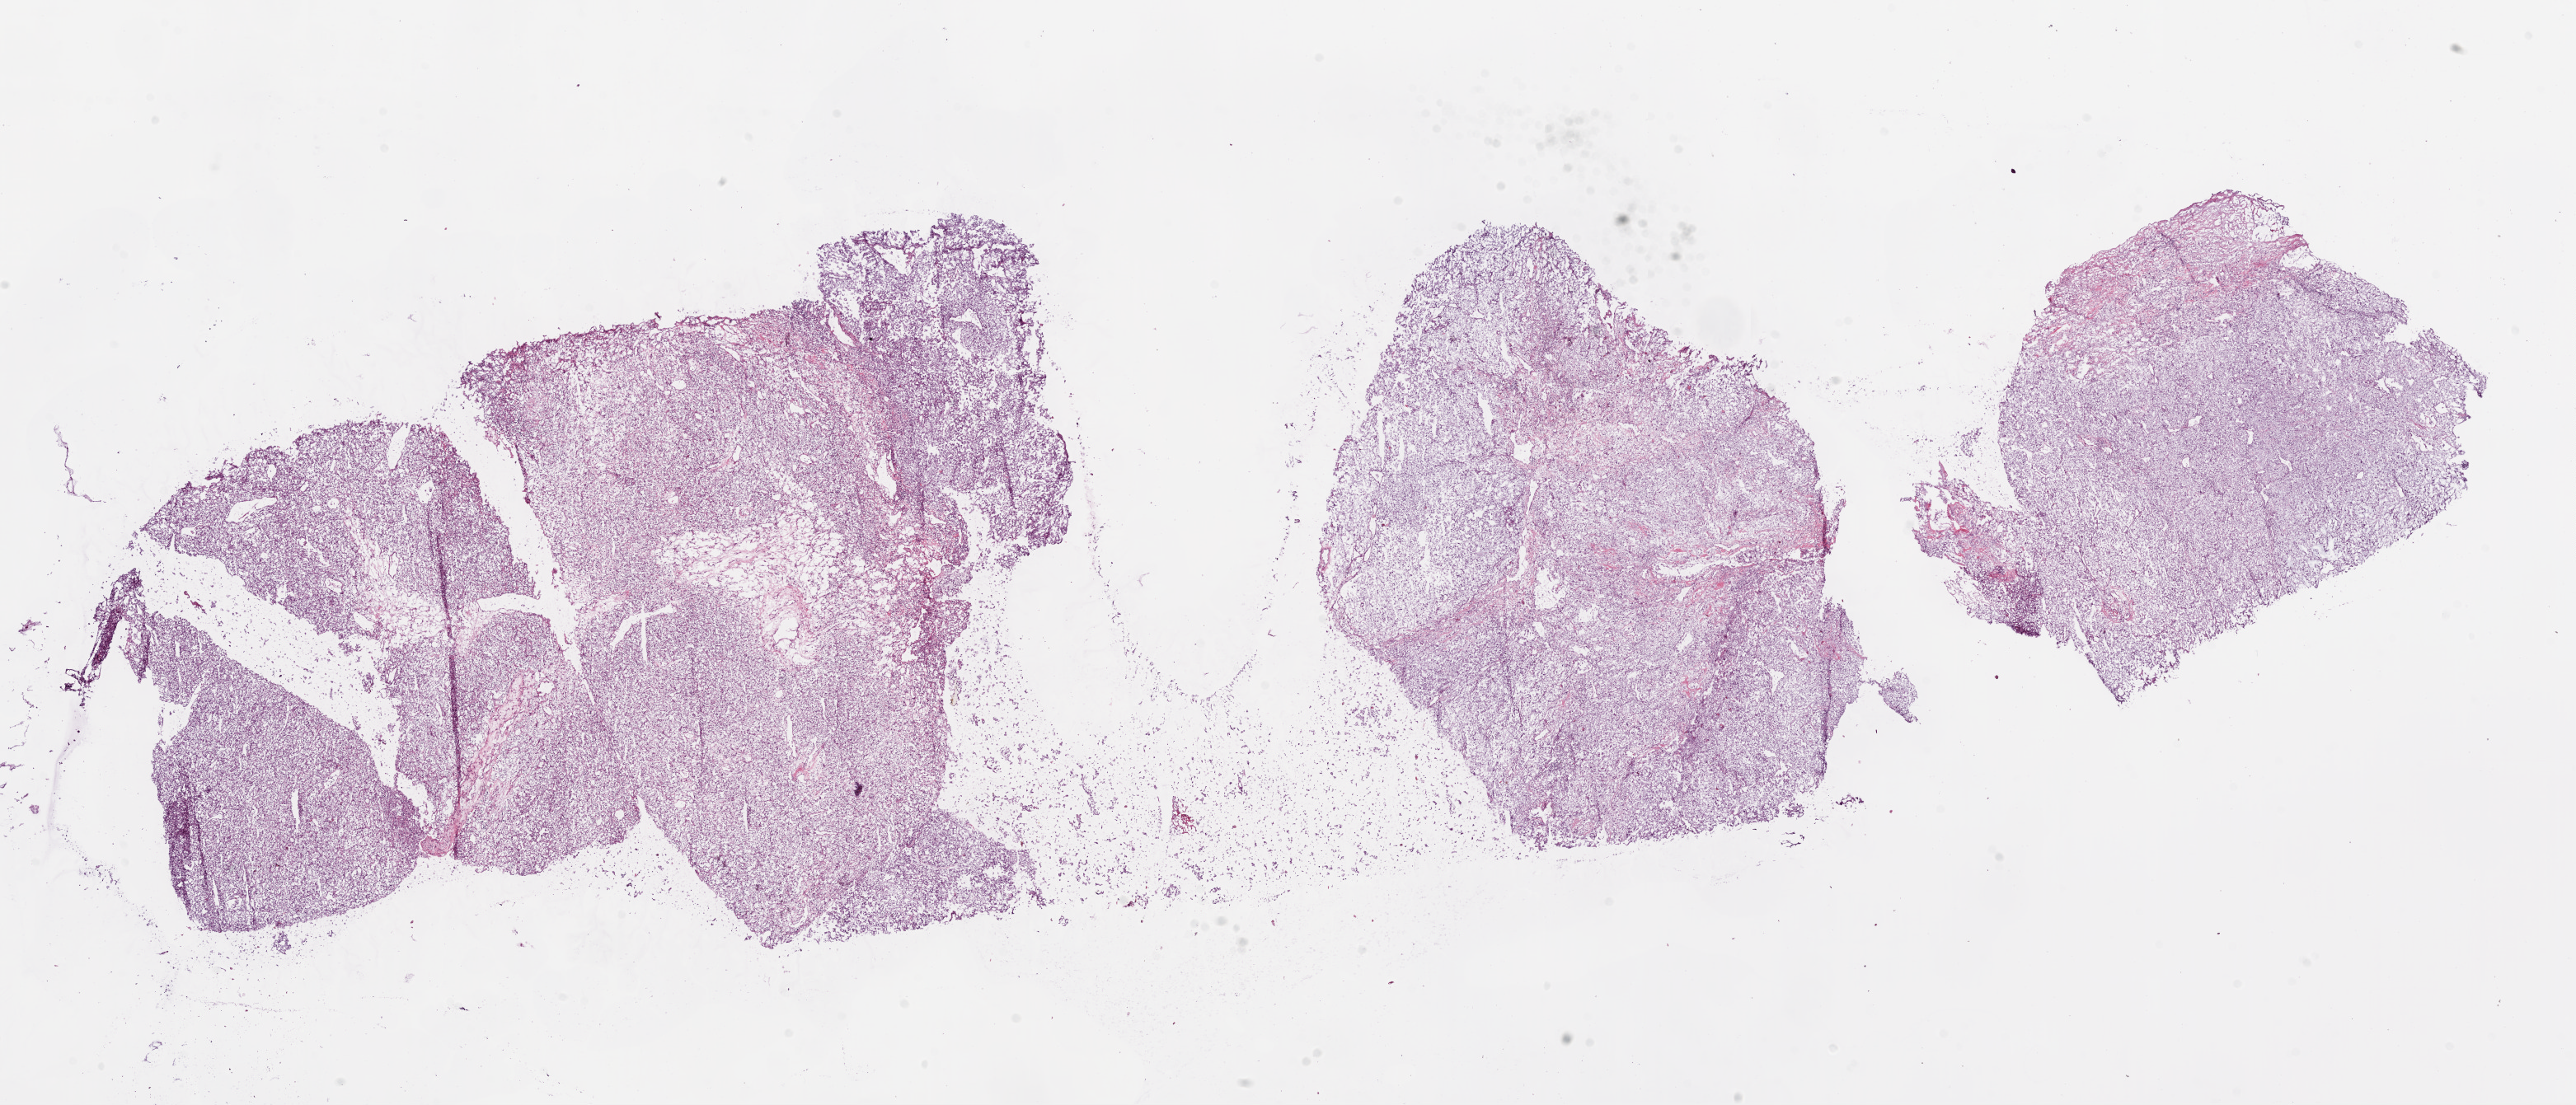
Hematoxylin and eosin (H&E) stained whole-slide image — whole scanned area (about 25.1 x 10.8 mm, slide scanned at 20x) shown as a low-resolution overview; frozen section; sample: primary tumour, kidney. Patient: female, age at initial diagnosis 64 years. Composition of this section per pathologist review: tumour cells 90%, tumour nuclei 85%.
Histologic diagnosis: Clear cell adenocarcinoma, NOS.